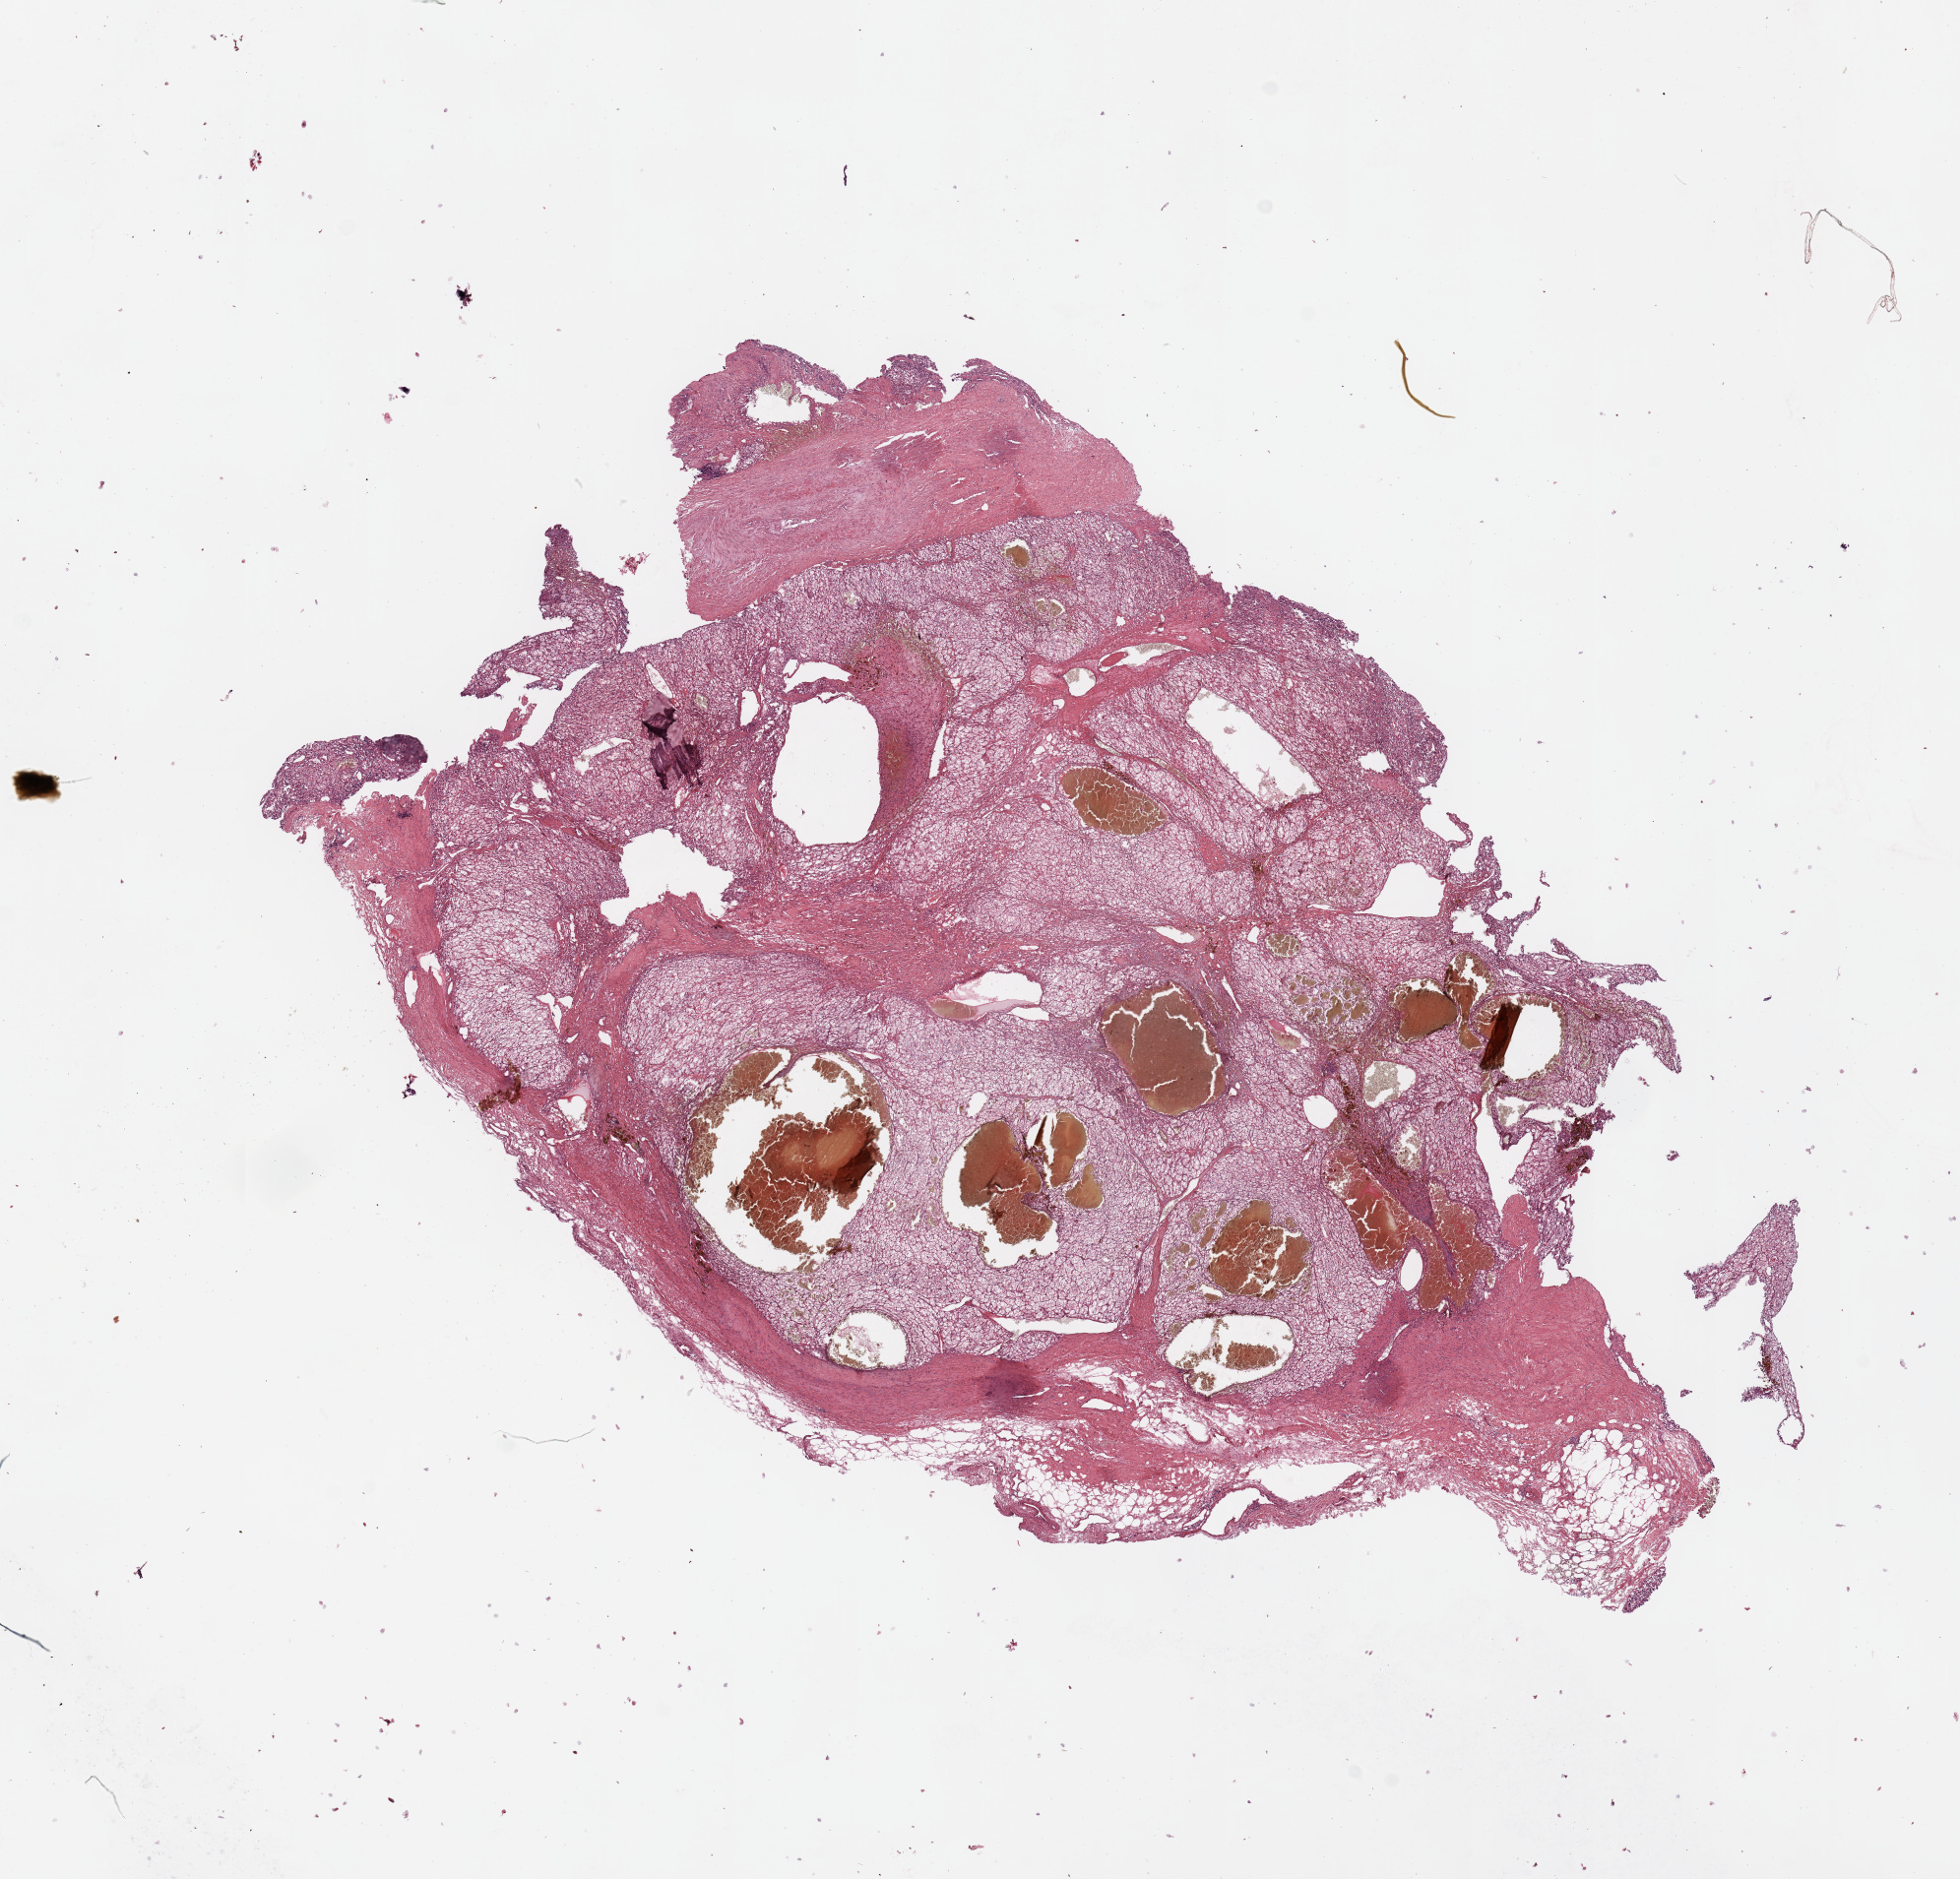
Whole-slide histology image, Hematoxylin and eosin (H&E) stained — a low-resolution overview of the entire scanned area, about 15.8 x 15.1 mm (slide scanned at 20x); kidney, tumour tissue. Female, 67 y/o.
Histologic diagnosis: Renal cell carcinoma, NOS.